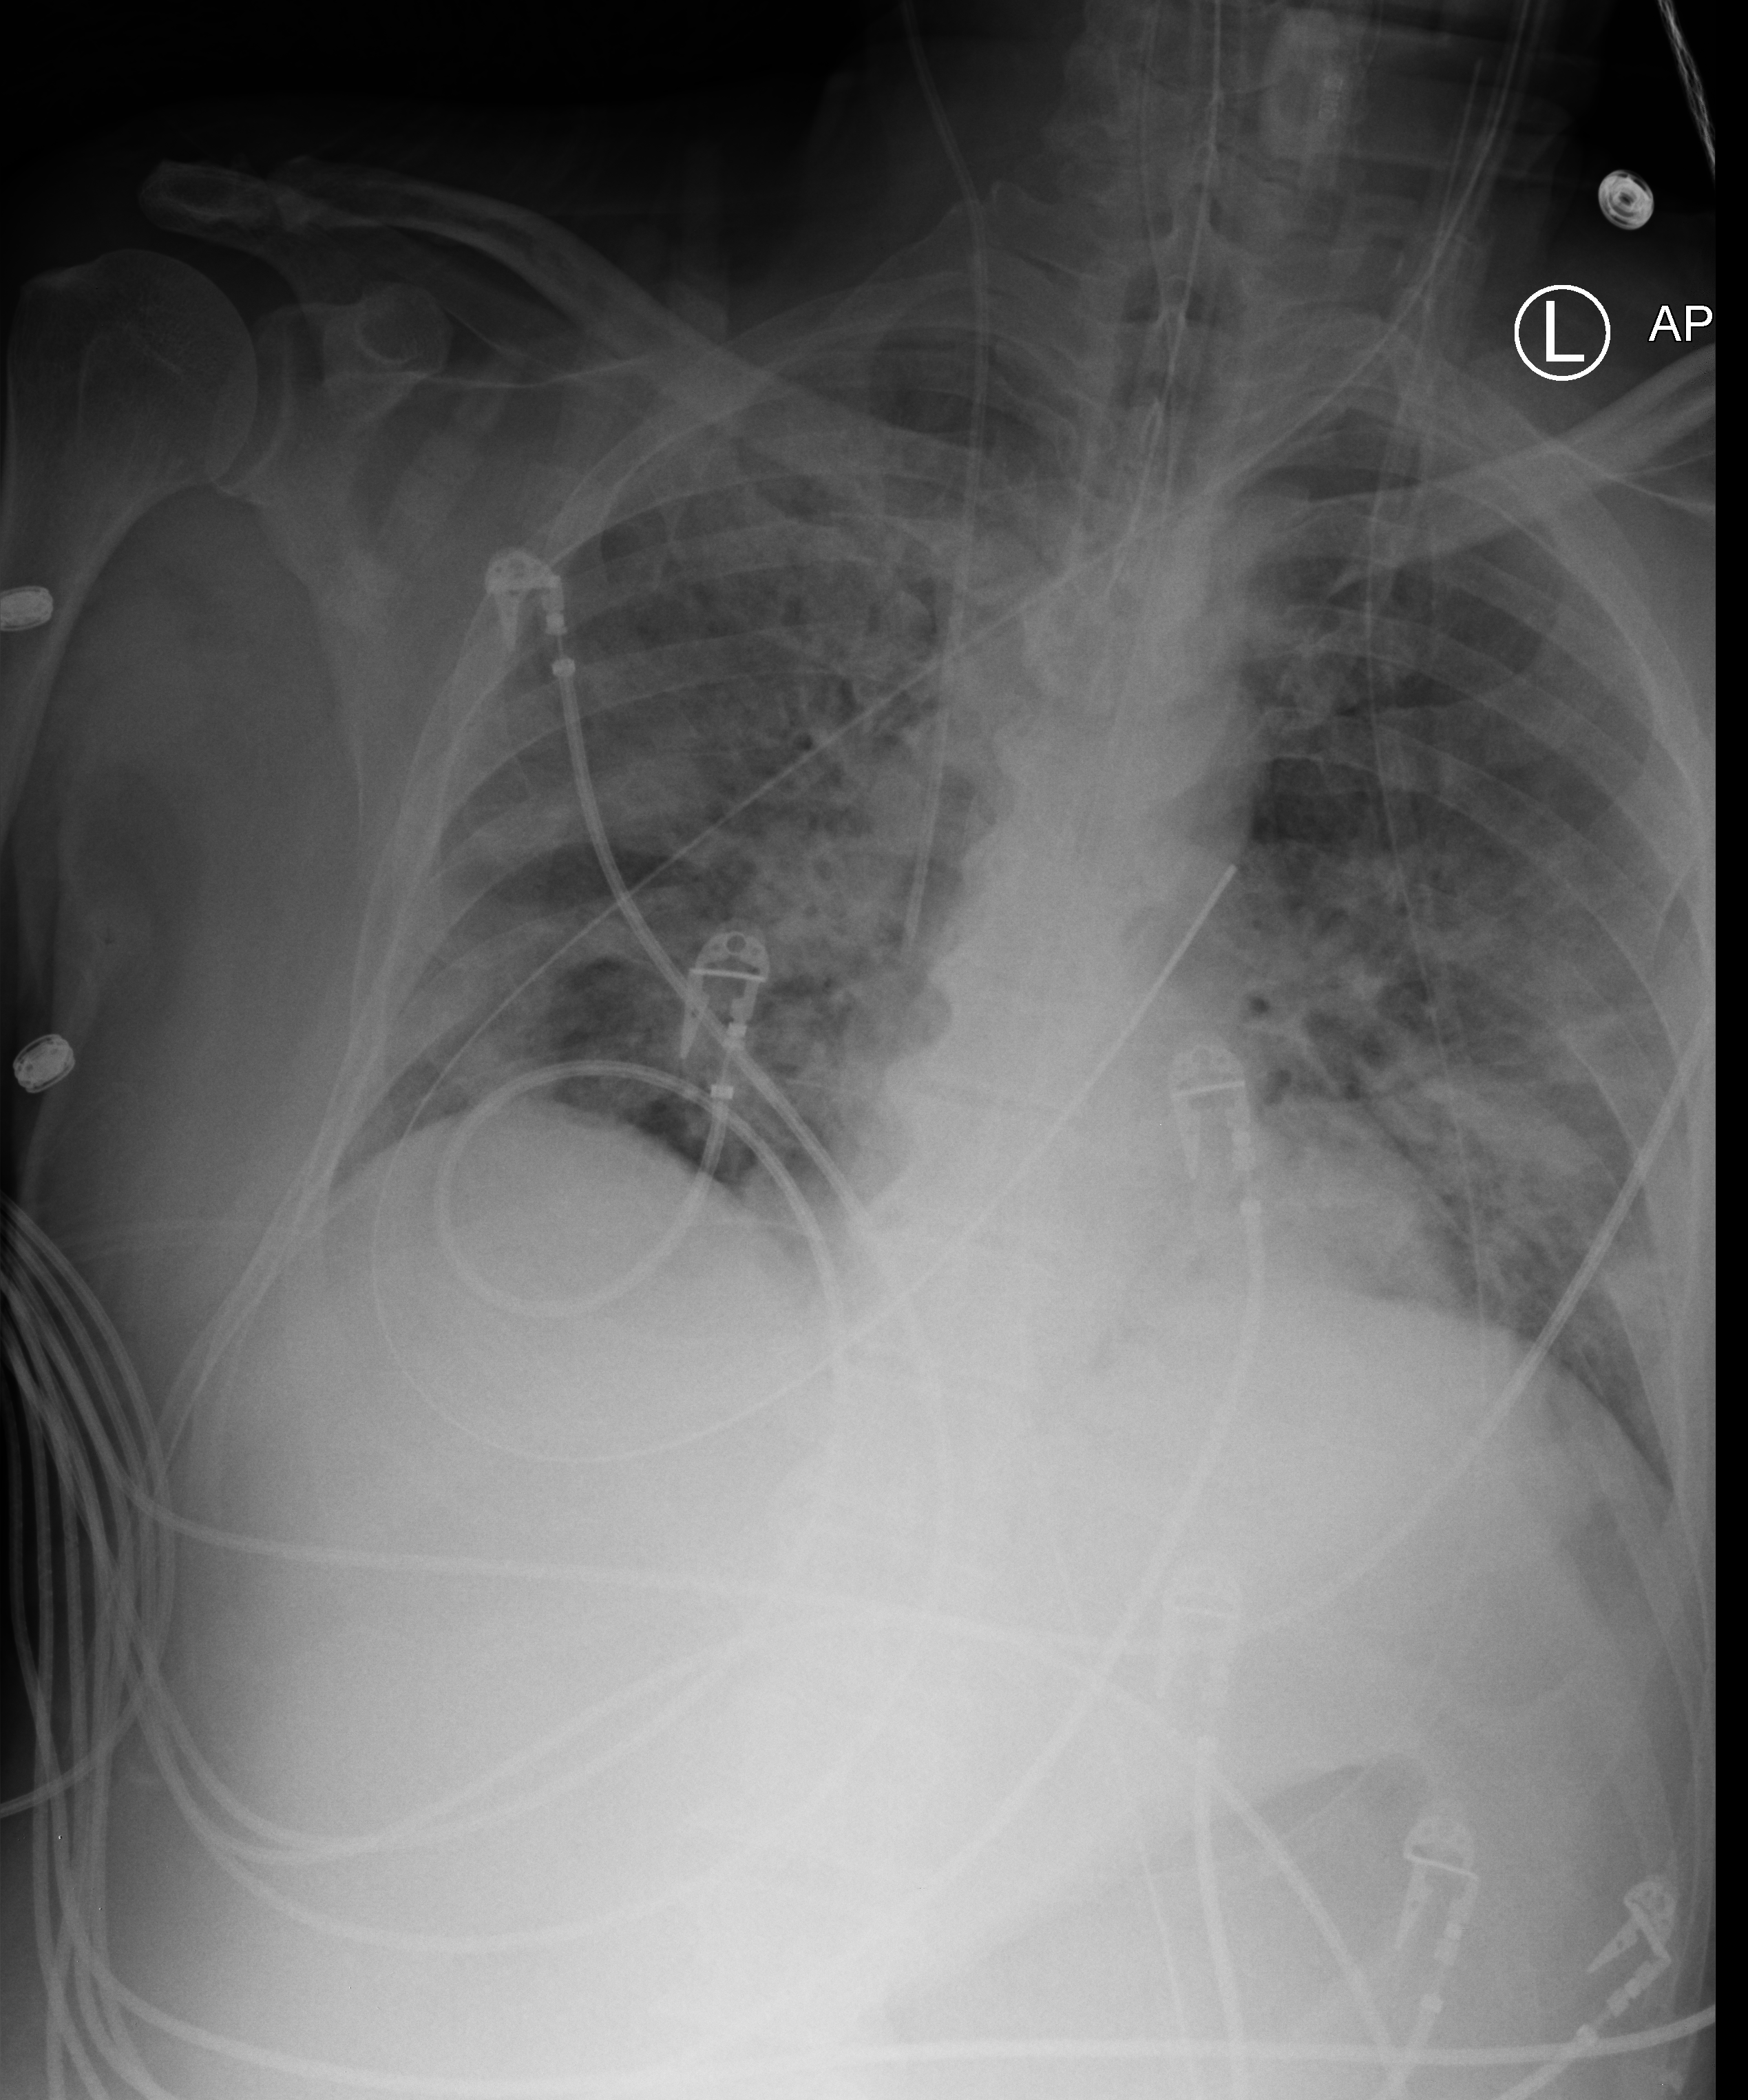
Chest X-ray (portable); anteroposterior (AP) projection. Male patient hospitalised with COVID-19, age 60–74 years.
Hospital-stay facts (about this admission, not read from this image; timing relative to this image not recorded): length of hospital stay: 15 days.